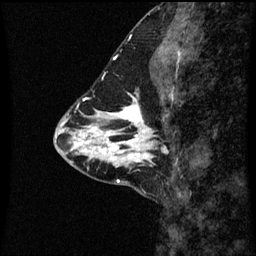
Breast MRI (dynamic contrast-enhanced), one sagittal slice. Slice 23 of 60 in the series (ordered by position). Dynamic contrast-enhanced series, image 2 of 3 at this slice position (ordered by acquisition). 1.5 T. TE 4.2 ms, TR 8.9 ms. 256 × 256 image matrix, field of view 200 × 200 mm. Patient: female, 43 years. From the clinical record (not read from this slice): setting: breast cancer imaged before/during neoadjuvant chemotherapy; receptor status: HR-positive, HER2-negative.
Annotated regions visible in this slice (semi-automatic segmentation, software-assisted and operator-edited):
- analysis volume of interest (the breast-tissue region the enhancement analysis was run in; not a lesion): bounding box (x1, y1, x2, y2) in pixels: (110, 100, 174, 163)
- tumour enhancement mask (voxels above the 70 % enhancement threshold inside the analysis volume of interest): (110, 100, 166, 163)